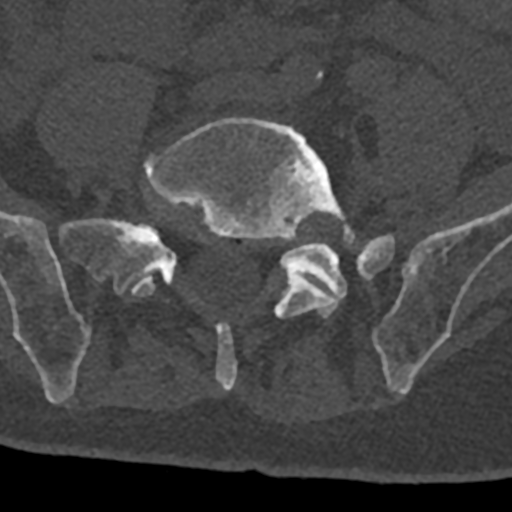
CT including the spine, one axial slice. Position 180 of 797 along the scan axis. 120 kVp. Bone window (W 1800 / L 400 HU). 0.5 mm slice thickness. 512 × 512 image matrix. Patient: male, 74 years. From the clinical record (not read from this slice): primary cancer: renal.
Annotated regions visible in this slice (semi-automatically segmented with operator editing):
- L4 vertebra: bounding box [x1, y1, x2, y2] px = [316, 71, 323, 81]
- L5 vertebra: [131, 117, 357, 391]